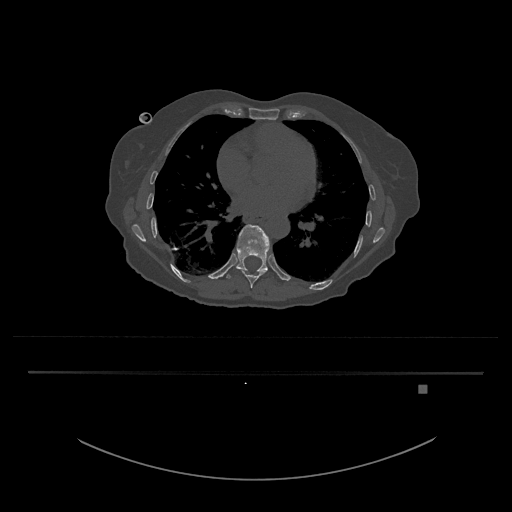
CT including the spine, one axial slice. Reconstruction kernel Br40s/3. 120 kVp. Bone window (W 1800 / L 400 HU). 0.5 mm slice thickness. 512 × 512 image matrix, field of view 500 × 500 mm. Patient: female, 57 years. Case-level facts recorded for this patient, not image findings: primary cancer: cervical.
Outlined on this slice (semi-automatically segmented with operator editing):
- T10 vertebra: box from (x=224, y=225) to (x=270, y=279) px
- T9 vertebra: (x=243, y=271)–(x=265, y=289)